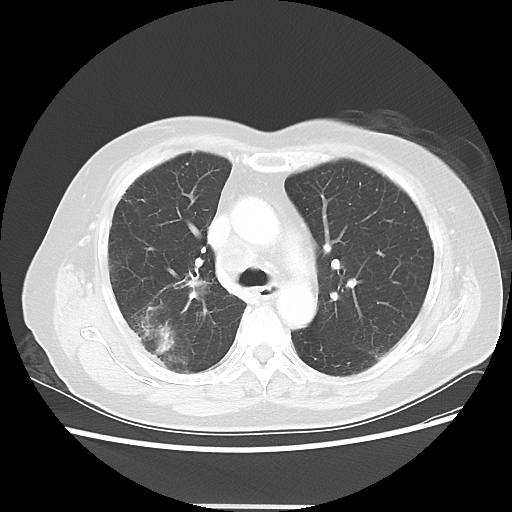
Chest CT, one axial slice; position 32 of 50 along the scan axis; reconstruction kernel LUNG; lung window (W 1500 / L -600 HU); 5 mm slice thickness; 512 × 512 image matrix, field of view 360 × 360 mm. Patient: female, 72 years. Case-level facts recorded for this patient, not image findings: clinical TNM (as recorded): T2 N1 M0; histopathological grade: G1.
Structures marked on this image (rectangle marked by the reading radiologist):
- lung tumour (recorded histology: adenocarcinoma): bounding box (x1, y1, x2, y2) in pixels: (139, 314, 176, 355)